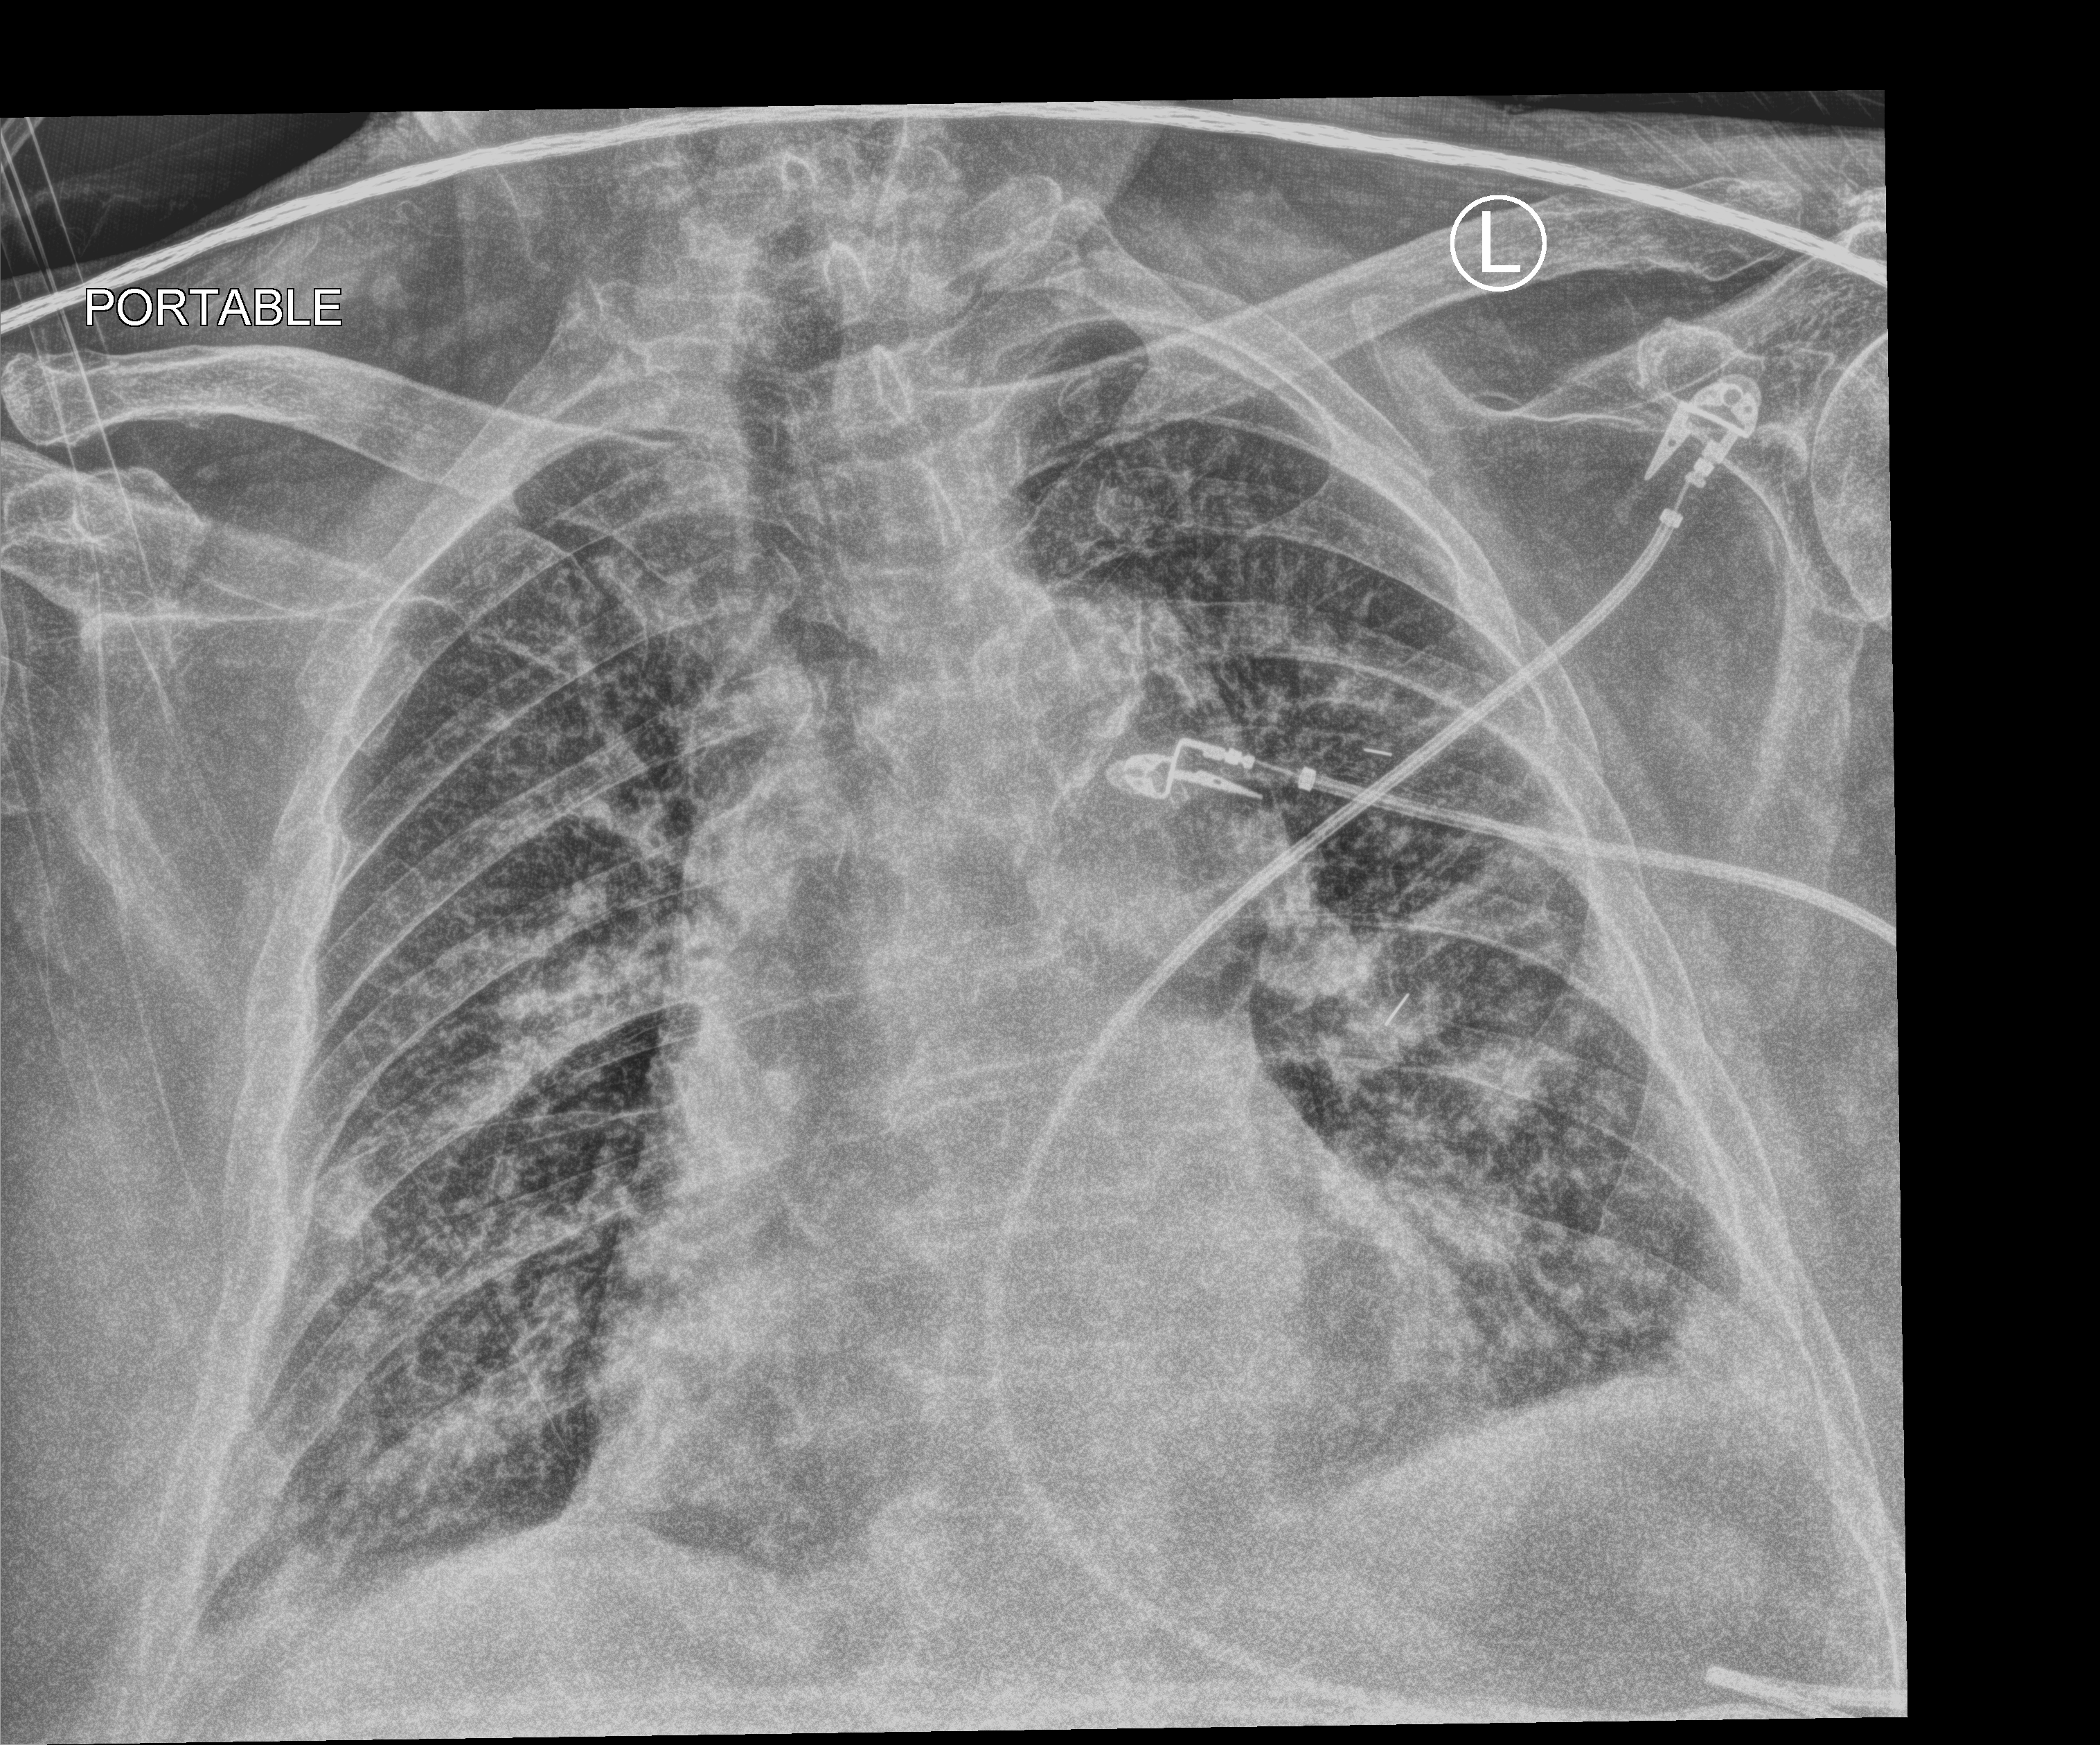
Portable chest radiograph, anteroposterior (AP) projection. Male patient hospitalised with COVID-19, age 75–90 years.
Hospital-stay facts (about this admission, not read from this image; timing relative to this image not recorded):
- admitted to intensive care during this hospital stay: no